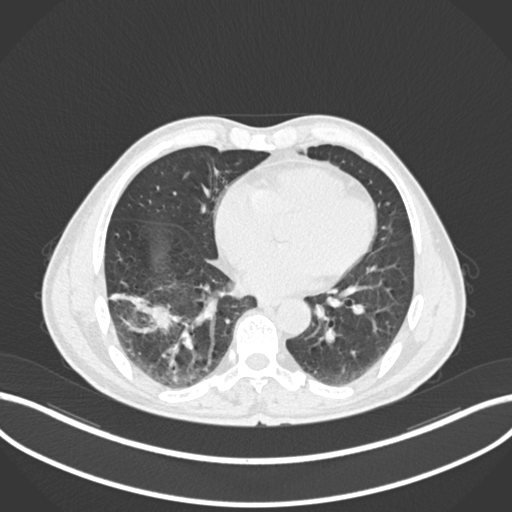
Chest CT, one axial slice. Slice 63 of 208 in the series (ordered by position). 120 kVp. Lung window (W 1500 / L -600 HU). 1 mm slice thickness. 512 × 512 image matrix, field of view 400 × 400 mm. Male patient, age 58 years. Case-level facts recorded for this patient, not image findings: clinical TNM (as recorded): T3 N0 M0; histopathological grade: G2.
Outlined on this slice (rectangle marked by the reading radiologist):
- lung tumour (recorded histology: squamous cell carcinoma): bounding box [x1, y1, x2, y2] px = [109, 282, 184, 342]